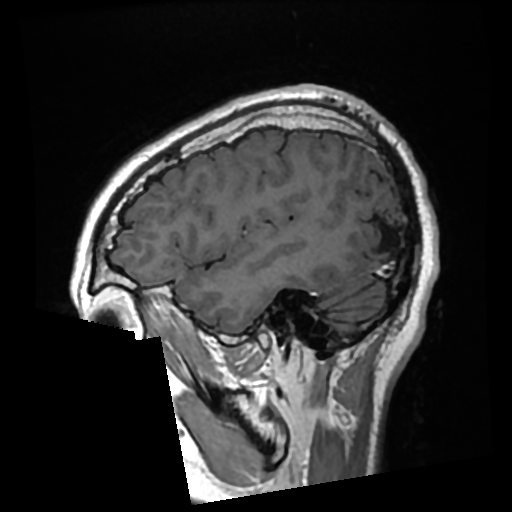
Brain MRI from a brain-tumour surgery series, one sagittal slice; position 76 of 276 along the scan axis; T1-weighted post-contrast; 0.7 mm slice thickness; 512 × 512 image matrix, field of view 250 × 250 mm. Case-level facts recorded for this patient, not image findings: histopathology: Glioma with ependymal features; WHO grade: 2; tumour location: Left Parietal.
Annotated regions visible in this slice (outlined manually by an expert reader):
- previous resection cavity: box from (x=367, y=220) to (x=395, y=255) px